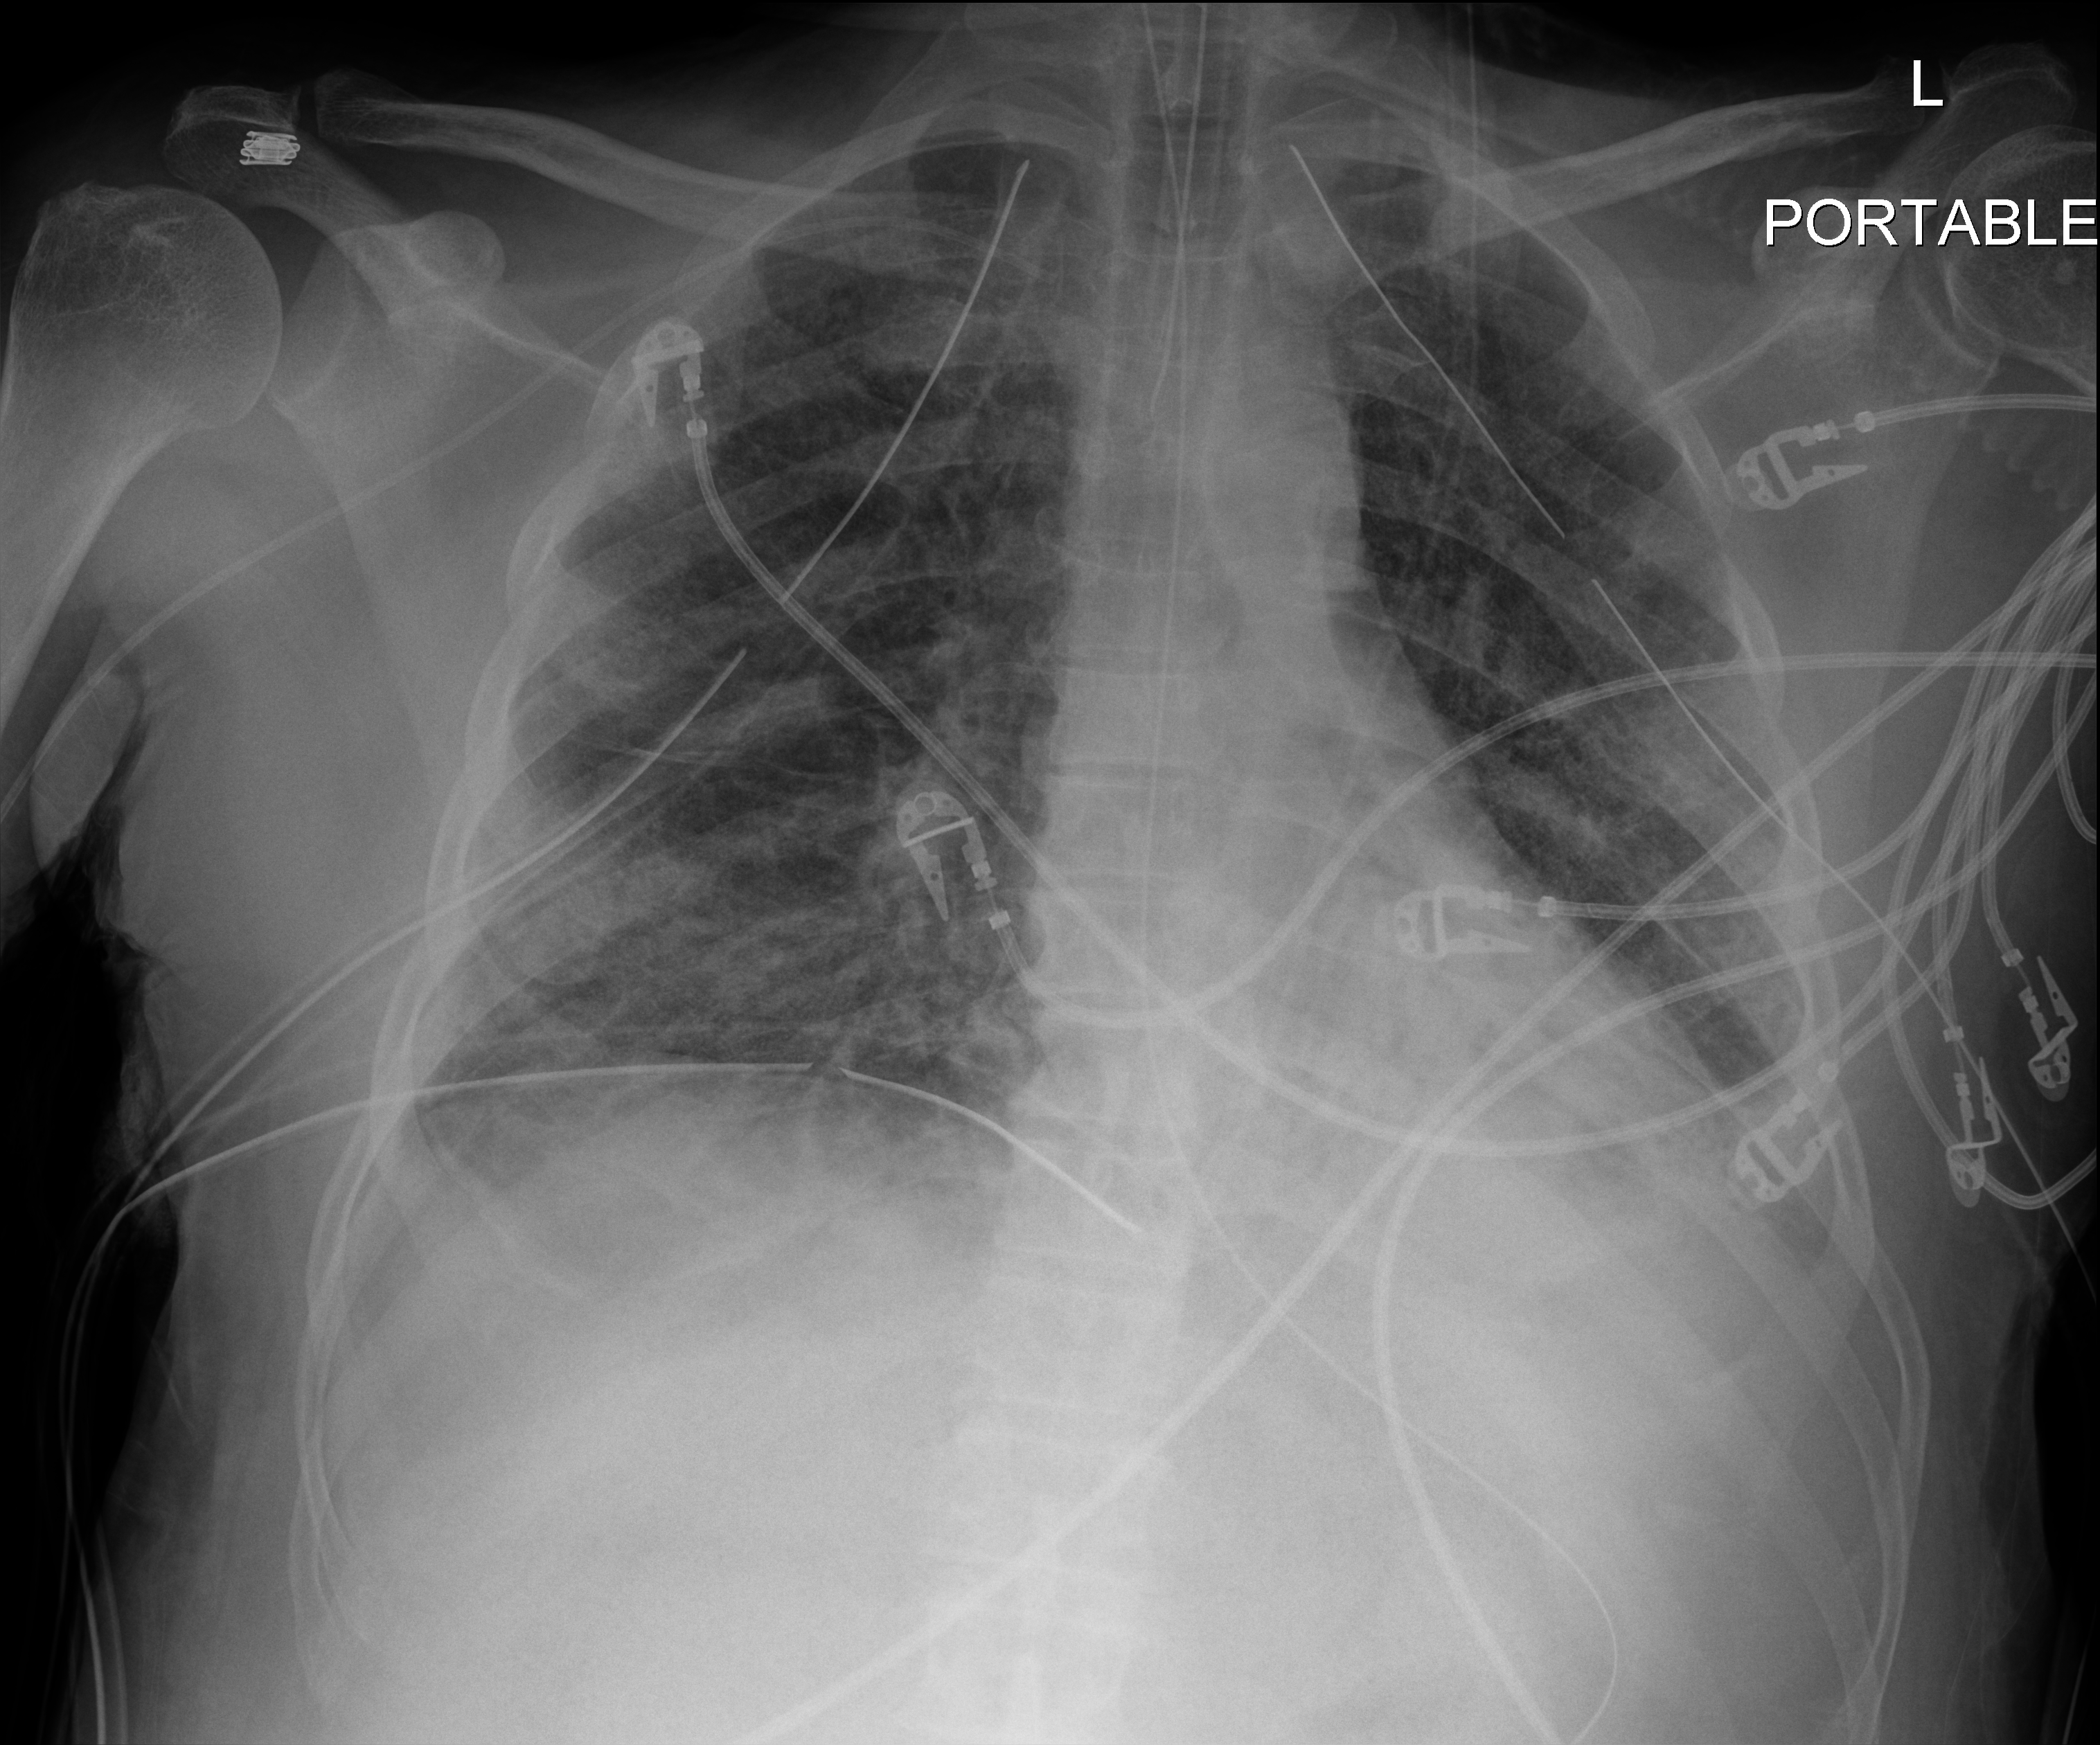
Bedside chest radiograph (digital radiography); anteroposterior (AP) projection. Patient hospitalised with COVID-19; male, aged 18–59 years.
Admission-level facts for this patient (not findings on this image; timing relative to this image not recorded): chronic kidney disease (admission record): no; admitted to intensive care during this hospital stay: yes.